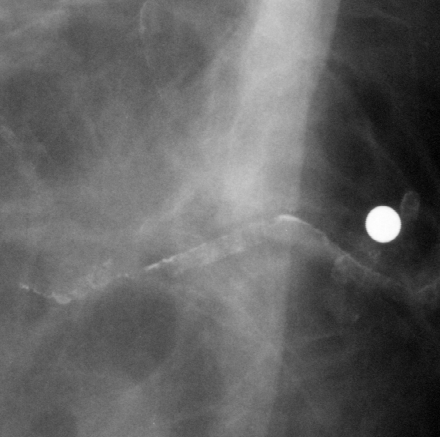
Region of interest cut from a scanned film mammogram (one marked finding), left breast, CC view.
Mass, shape irregular, margins ill defined; BI-RADS assessment category 5; subtlety rating 4 on a 1 (subtle) to 5 (obvious) scale; pathology (as recorded): malignant.